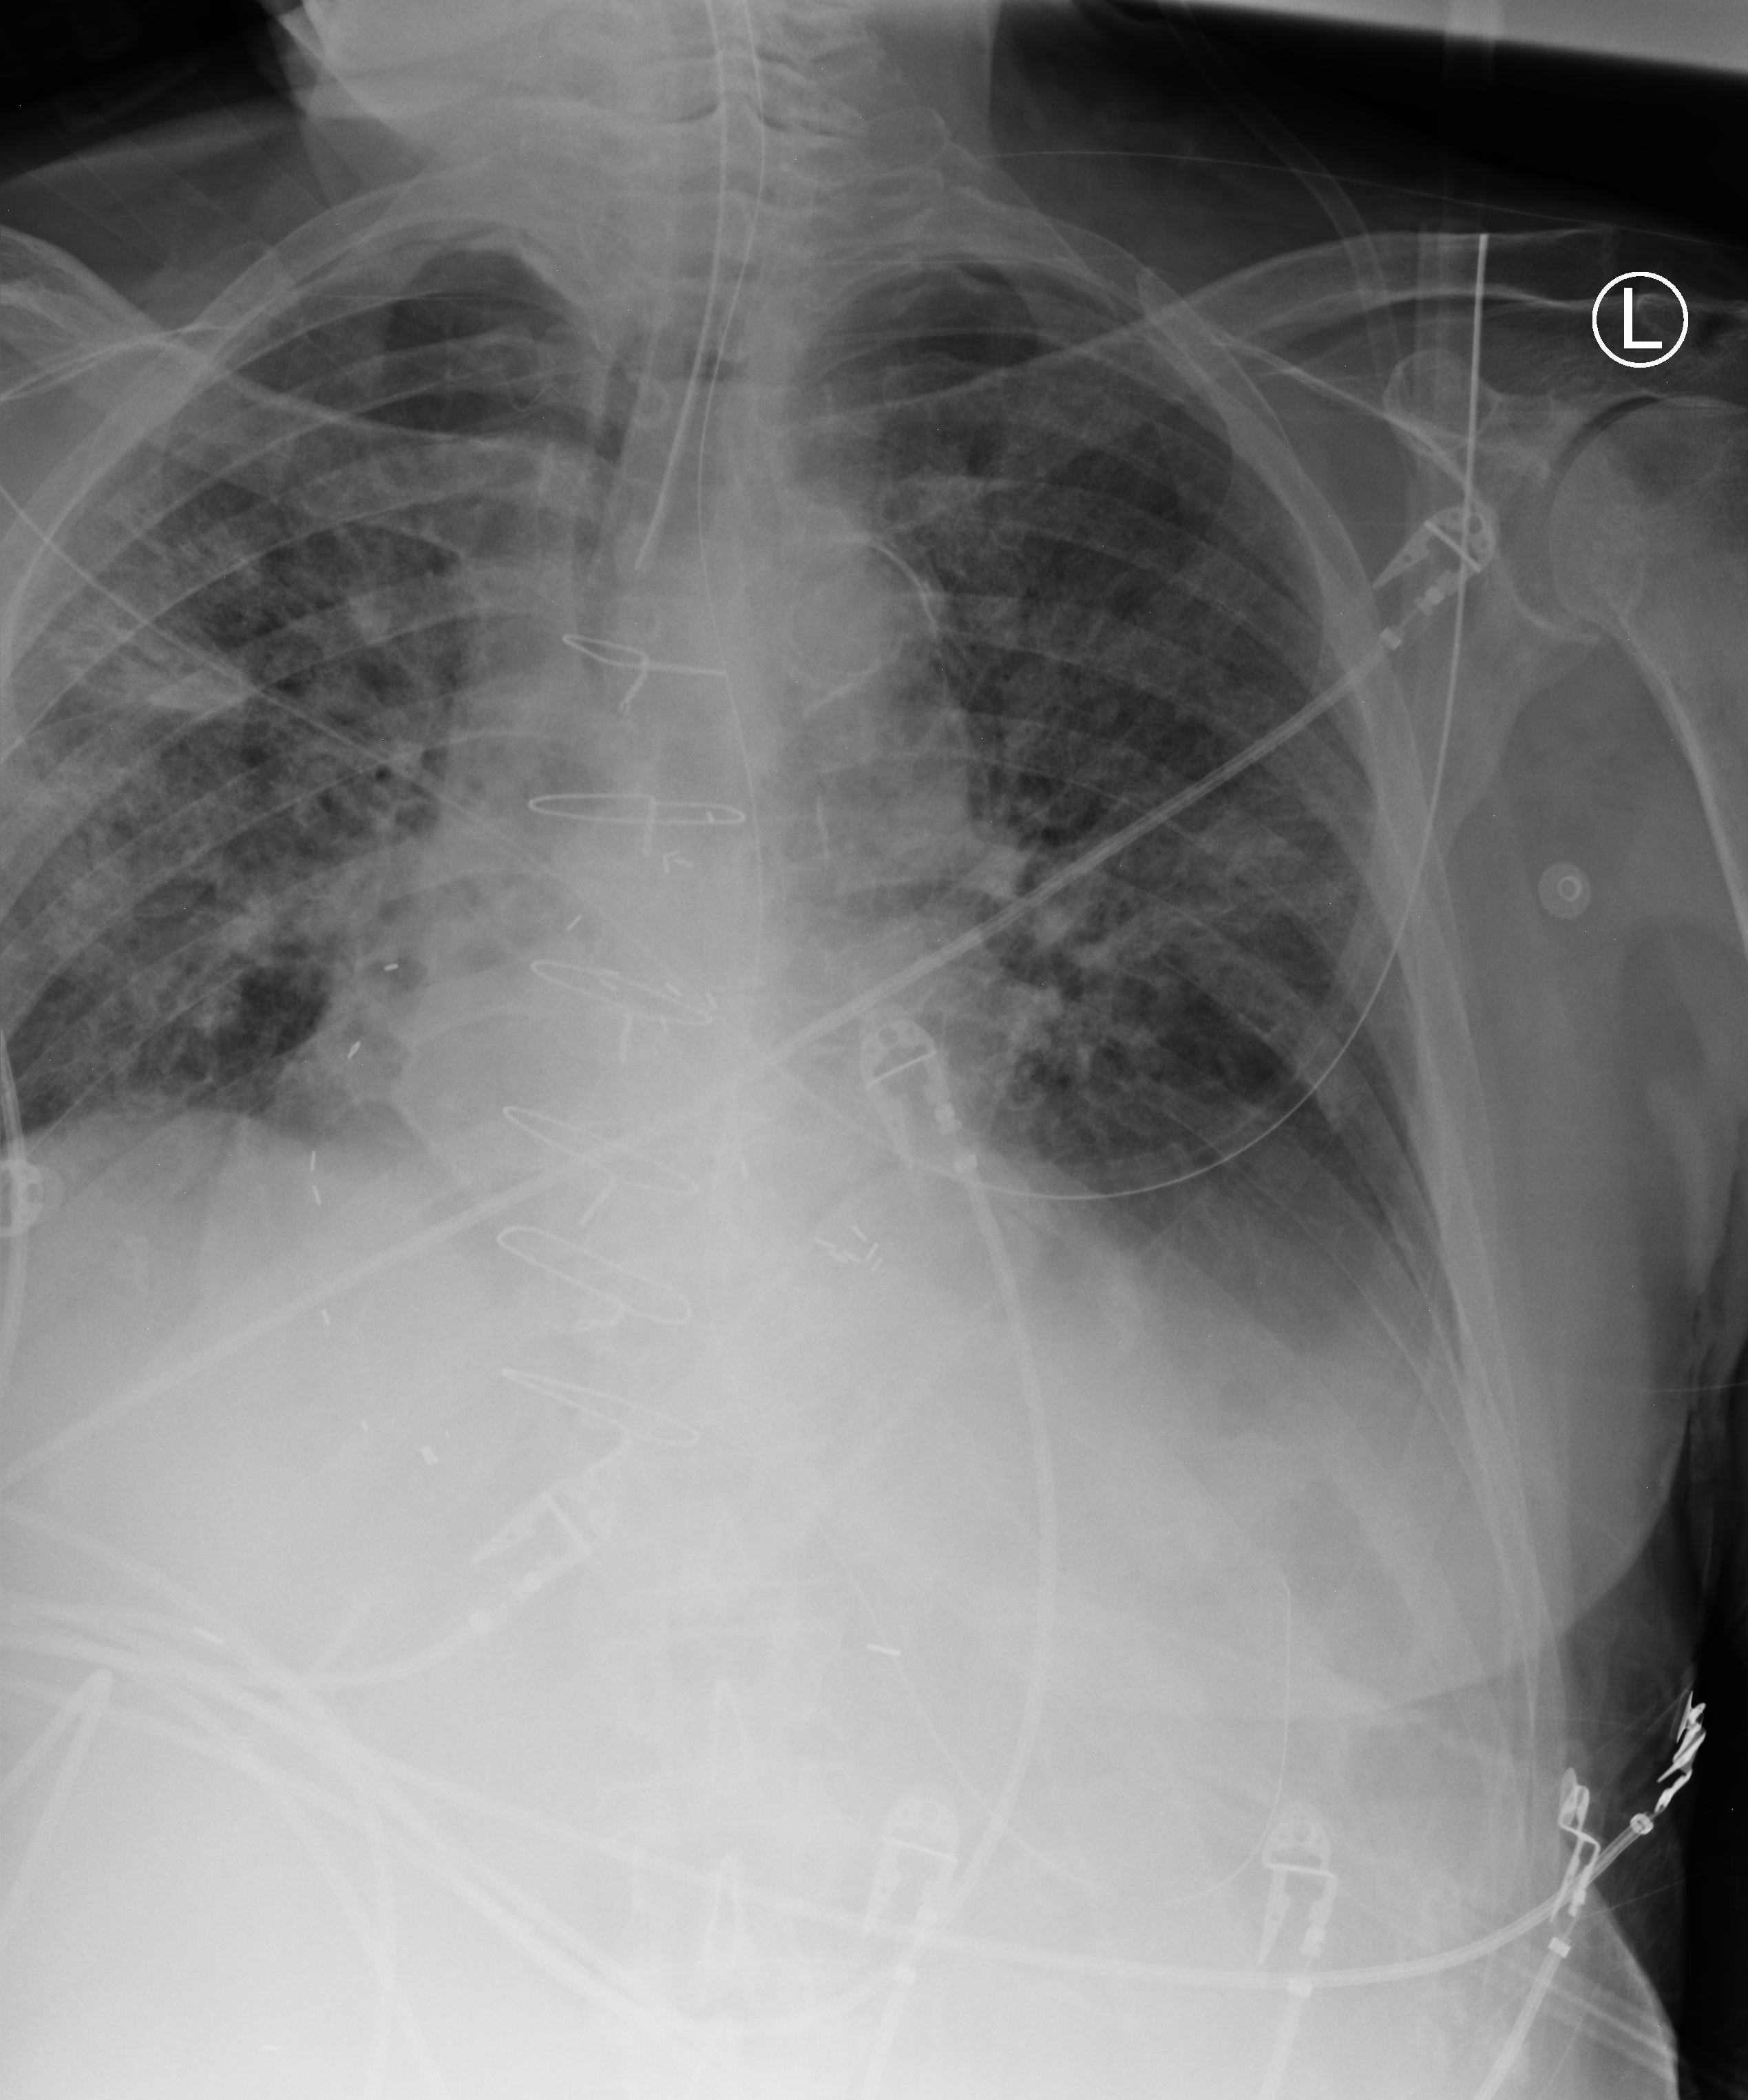
Portable chest radiograph; anteroposterior (AP) projection. Male patient hospitalised with COVID-19, age 75–90 years.
From the hospital-stay record, not from the radiograph (when in the stay this image was taken is not recorded):
- mechanically ventilated during this hospital stay: yes
- admitted to intensive care during this hospital stay: yes